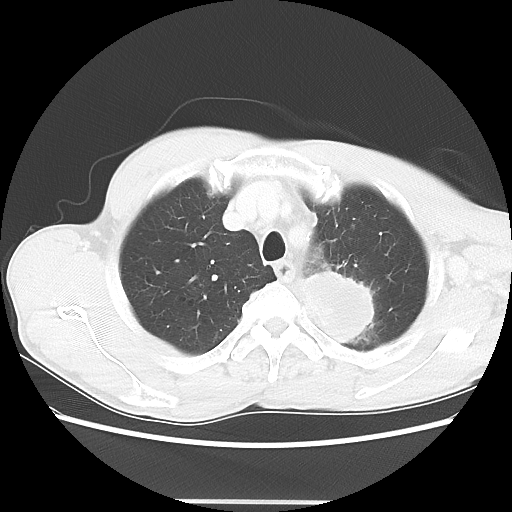
Chest CT, one axial slice; position 53 of 62 along the scan axis; reconstruction kernel LUNG; 100 kVp; lung window (W 1500 / L -600 HU); 5 mm slice thickness; 512 × 512 image matrix, field of view 360 × 360 mm. Male patient, age 61 years. Case-level facts recorded for this patient, not image findings: clinical TNM (as recorded): T3 N1 M1.
Outlined on this slice (rectangle marked by the reading radiologist):
- lung tumour (recorded histology: adenocarcinoma): box from (x=298, y=263) to (x=382, y=352) px